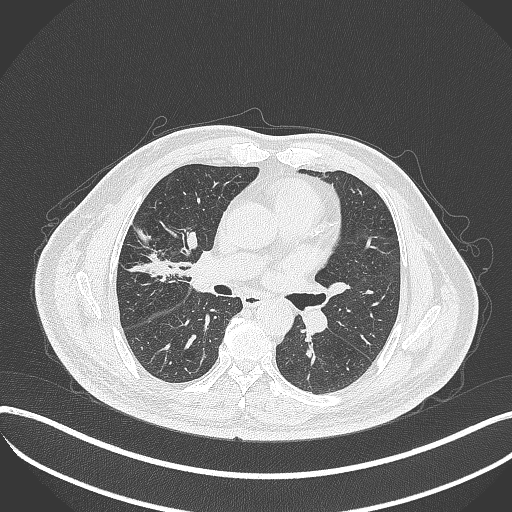
Chest CT, one axial slice. Position 198 of 401 along the scan axis. Reconstruction kernel B70f. 120 kVp. Lung window (W 1500 / L -600 HU). 1 mm slice thickness. 512 × 512 image matrix. Patient: male, 72 years. Case-level facts recorded for this patient, not image findings: clinical TNM (as recorded): T1c N0 M0.
Structures marked on this image (rectangle marked by the reading radiologist):
- lung tumour (recorded histology: squamous cell carcinoma): bounding box <173,246,216,293> (left, top, right, bottom; pixels)